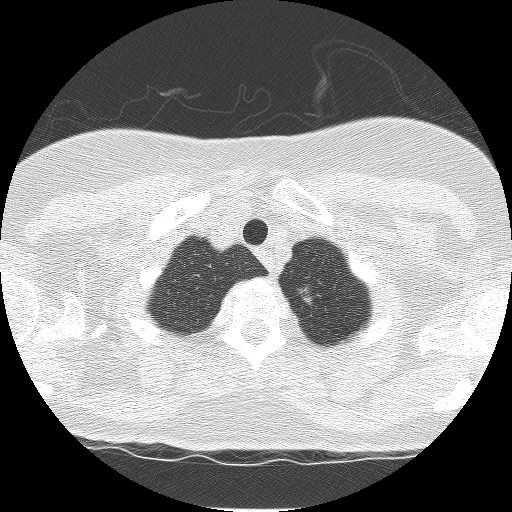
Axial slice from a low-dose chest CT screening exam. Third screening round (two years after baseline). Lung window (W 1500 / L -600 HU). Lung (sharp) reconstruction kernel (BONE). Slice 9 of 120 in the series. 512 × 512 image matrix. Female, age 59 years at enrolment. Former smoker at enrolment.
• Expert reader's lesion annotation, bounding box [x1, y1, x2, y2] px = [281, 272, 334, 318].
• The screening reader recorded 3 non-calcified nodules or masses ≥4 mm on this exam; which of them this box marks is not recorded.
• Lung cancer was diagnosed 42 days after this screen: bronchiolo-alveolar adenocarcinoma, NOS, left upper lobe, well differentiated (G1), stage IA (AJCC 6th edition), 10 mm at pathology.